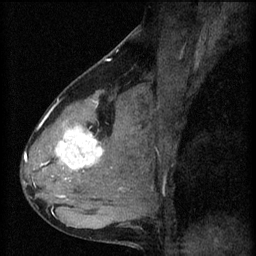
Breast MRI (dynamic contrast-enhanced), one sagittal slice; slice 37 of 60 in the series (ordered by position); 3 images stored at this slice position (order not interpretable as contrast timing); 1.5 T; TE 4.2 ms, TR 8.2 ms; 2 mm slice thickness; 256 × 256 image matrix, field of view 180 × 180 mm. Female patient, age 37 years.
Annotated regions visible in this slice (semi-automatically segmented with operator editing):
- analysis volume of interest (the breast-tissue region the enhancement analysis was run in; not a lesion): bounding box (x1, y1, x2, y2) in pixels: (44, 100, 119, 197)
- tumour enhancement mask (voxels above the 70 % enhancement threshold inside the analysis volume of interest): (56, 102, 105, 197)